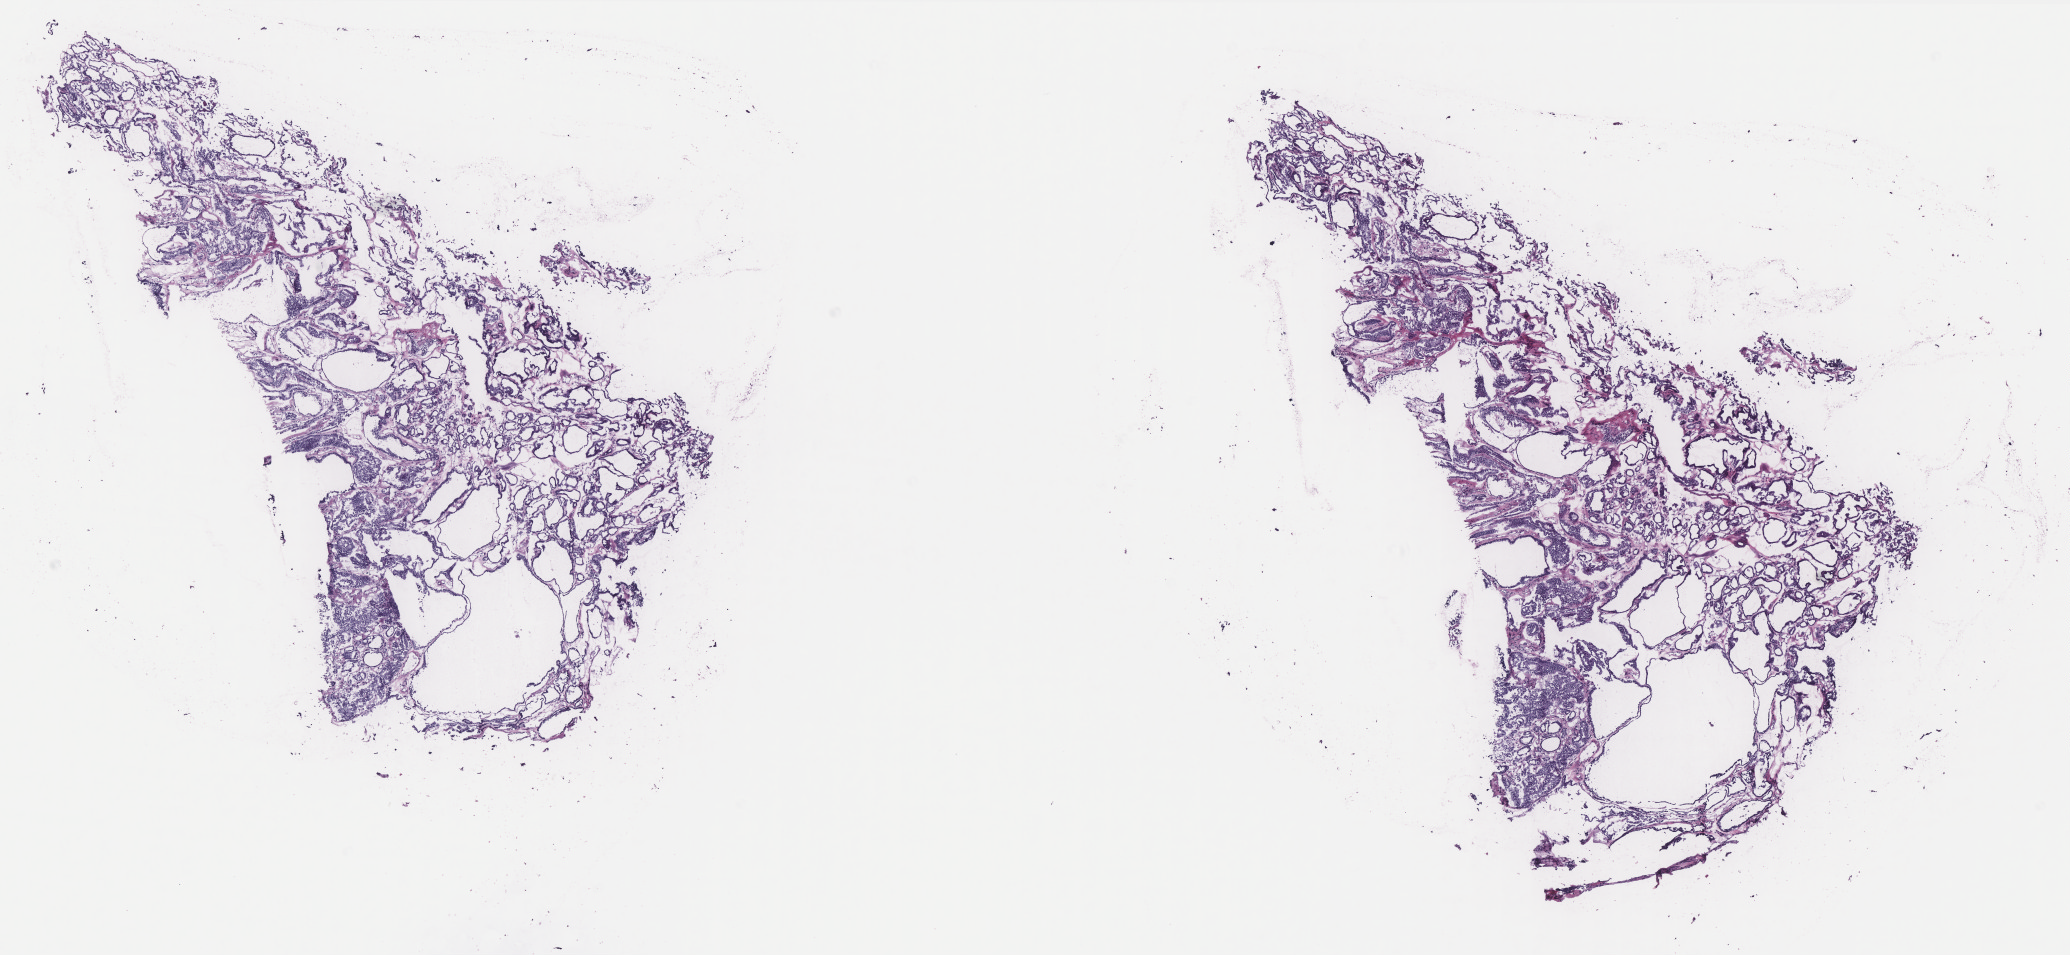
Hematoxylin and eosin (H&E) stained whole-slide image, whole scanned area (about 16.6 x 7.7 mm) shown as a low-resolution overview. Frozen section from the top of the tissue portion. Sample: primary tumour, thyroid. Male patient; age at initial diagnosis 55 years. Pathologist review of this section (percent, as recorded): tumour cells 100%, tumour nuclei 80%, normal cells 0%, stromal cells 0%, necrosis 0%. Infiltration values recorded for this section: lymphocyte infiltration 0%, monocyte infiltration 0%, neutrophil infiltration 0%.
Histologic diagnosis: Papillary adenocarcinoma, NOS (thyroid gland). AJCC pathologic stage: I (7th edition).